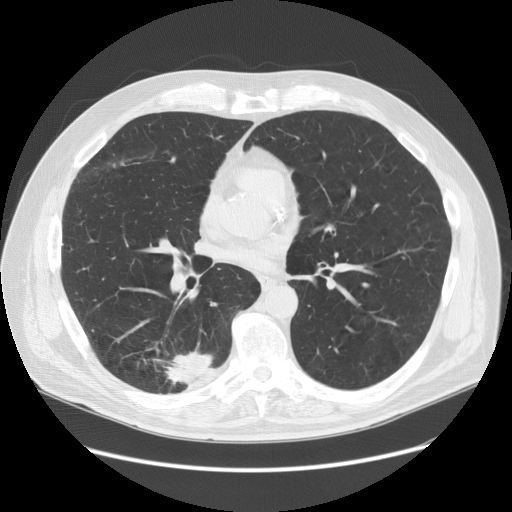
Low-dose screening chest CT, one axial slice; position 72 of 149 along the scan axis; reconstruction kernel STANDARD; 120 kVp; lung window (W 1500 / L -600 HU); 2.5 mm slice thickness; 512 × 512 image matrix, field of view 400 × 400 mm.
Outlined on this slice (manually delineated by an expert):
- lesion 1 (tumor, lower lobe of right lung): bounding box (x1, y1, x2, y2) in pixels: (163, 350, 214, 385)